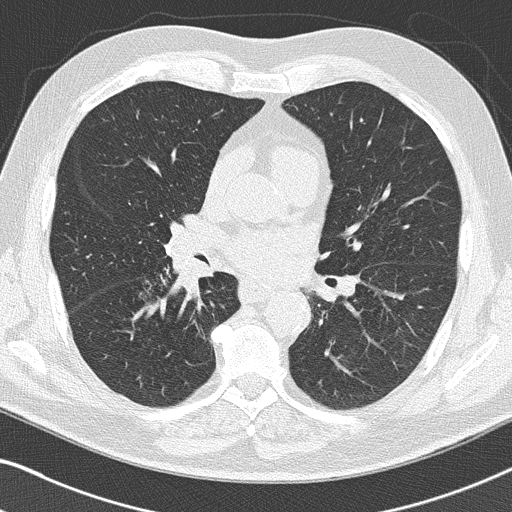
Low-dose screening chest CT, axial slice. Third screening round (two years after baseline). Lung window (W 1500 / L -600 HU). 2 mm slice thickness. 120 kVp. 512 × 512 image matrix. Male, age 66 years at enrolment.
- Lesion marked by an expert reader, box from (x=134, y=269) to (x=228, y=333) px.
- Screening reader's record for this exam (one nodule recorded; not confirmed to be the boxed lesion): non-calcified nodule or mass ≥4 mm, right upper lobe, 5 × 4 mm, smooth margins, pre-existing on the prior screen: yes; interval growth: no.
- Official screen result: positive, other.